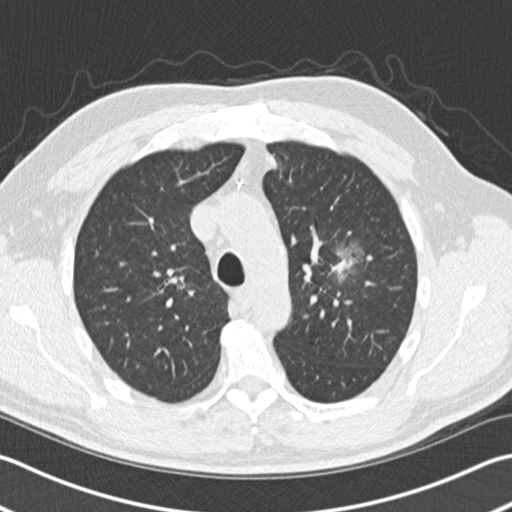
Low-dose screening chest CT, one axial slice; lung window (W 1500 / L -600 HU); 2 mm slice thickness; 512 × 512 image matrix, field of view 346 × 346 mm.
Outlined on this slice (outlined manually by an expert reader):
- lesion 1 (tumor, upper lobe of left lung): box from (x=332, y=259) to (x=352, y=276) px